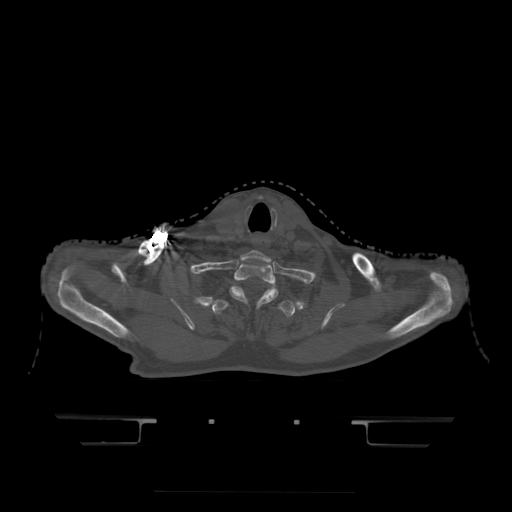
CT including the spine, one axial slice. Position 396 of 522 along the scan axis. Bone window (W 1800 / L 400 HU). 1.25 mm slice thickness. 512 × 512 image matrix, field of view 436 × 436 mm. Patient age 68 years. From the clinical record (not read from this slice): primary cancer: urothelial.
Structures marked on this image (semi-automatic segmentation, software-assisted and operator-edited):
- T1 vertebra: box from (x=230, y=263) to (x=278, y=304) px
- T2 vertebra: (x=213, y=288)–(x=295, y=335)